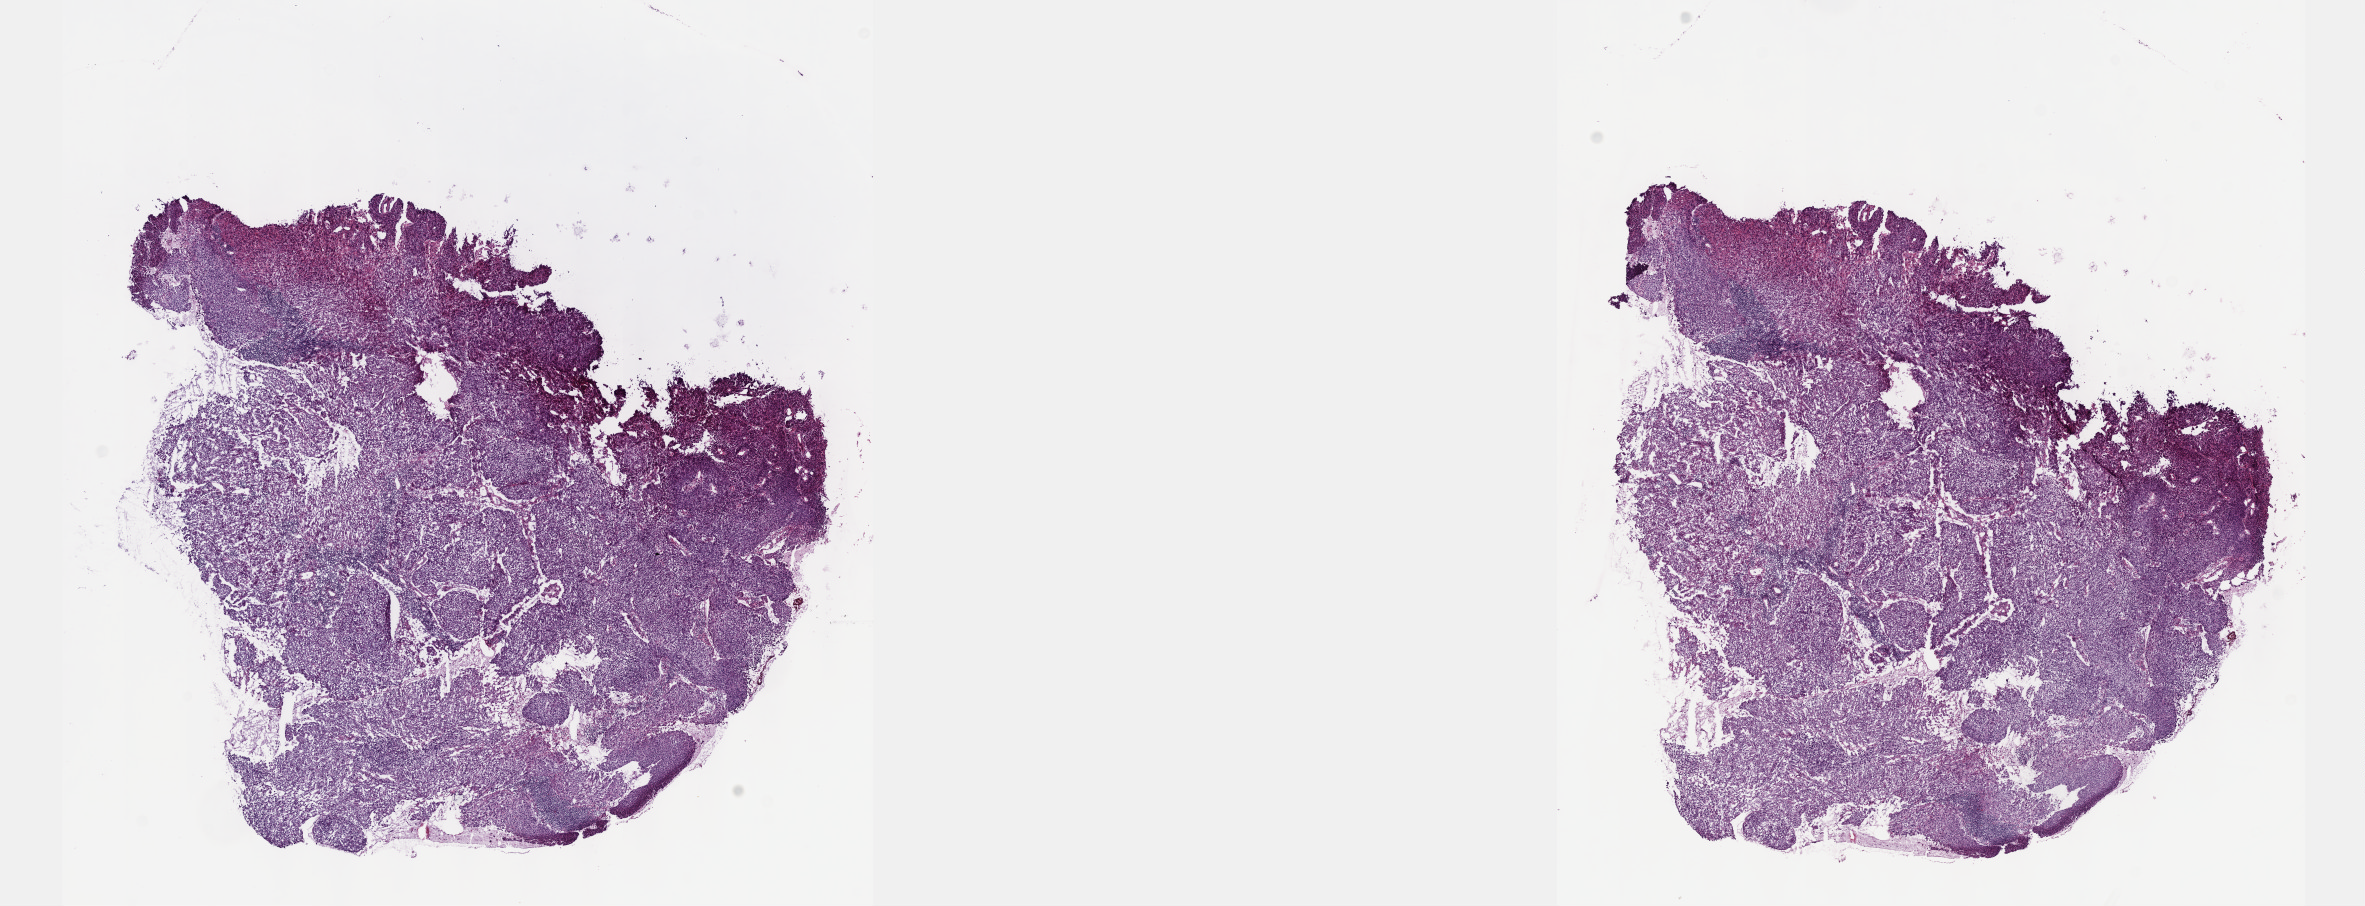
H&E whole-slide image, a low-resolution overview of the entire scanned area, about 19.1 x 7.3 mm; frozen section; cervix, primary tumour sample. Female patient; age at initial diagnosis 62 years. Histologic grade: G3 (poorly differentiated). Composition of this section per pathologist review: tumour cells 97%, tumour nuclei 80%, normal cells 0%, stromal cells 0%, necrosis 3%. Infiltration values recorded for this section: lymphocyte infiltration 3%, monocyte infiltration 0%, neutrophil infiltration 0%.
Diagnosis: Squamous cell carcinoma, NOS (cervix uteri). FIGO stage: IVB.